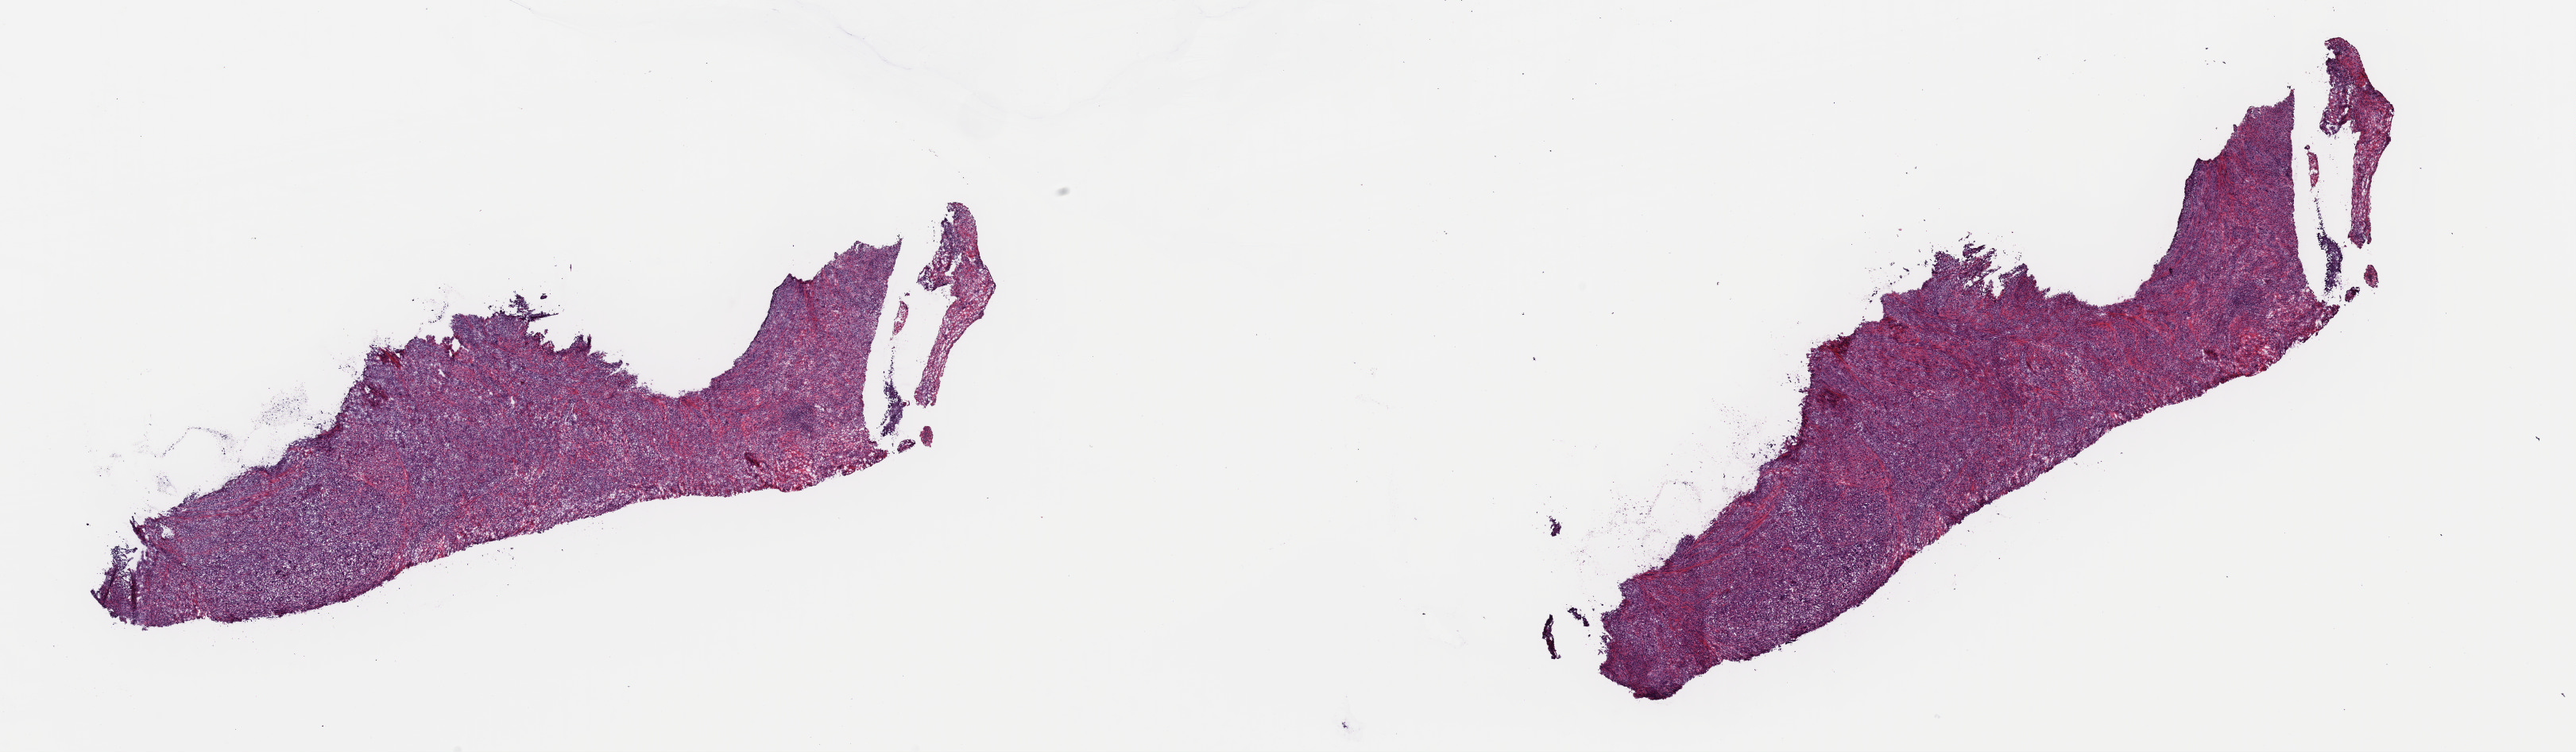
Digitized H&E tissue section (whole slide) — a low-resolution overview of the entire scanned area, about 25.6 x 7.5 mm (from a 40x scan); frozen section from the top of the tissue portion; metastatic tumour sample, sampled site not recorded. Patient: female, age at initial diagnosis 64 years. Composition of this section per pathologist review: tumour cells 100%, tumour nuclei 65%, normal cells 0%, stromal cells 0%, necrosis 0%. Inflammatory infiltration, as recorded: lymphocyte infiltration 0%, monocyte infiltration 0%, neutrophil infiltration 0%.
This section: metastatic tumour tissue. Patient diagnosis: Malignant melanoma, NOS.